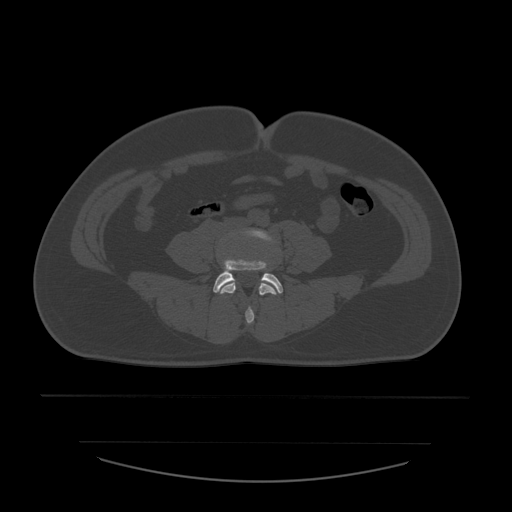
CT including the spine, one axial slice. Position 133 of 532 along the scan axis. Bone window (W 1800 / L 400 HU). 1.25 mm slice thickness. 512 × 512 image matrix. Patient age 44 years. Case-level facts recorded for this patient, not image findings: primary cancer: soft tissue sarcoma.
Structures marked on this image (semi-automatically segmented with operator editing):
- L4 vertebra: box from (x=220, y=229) to (x=281, y=324) px
- L5 vertebra: (x=213, y=260)–(x=283, y=294)